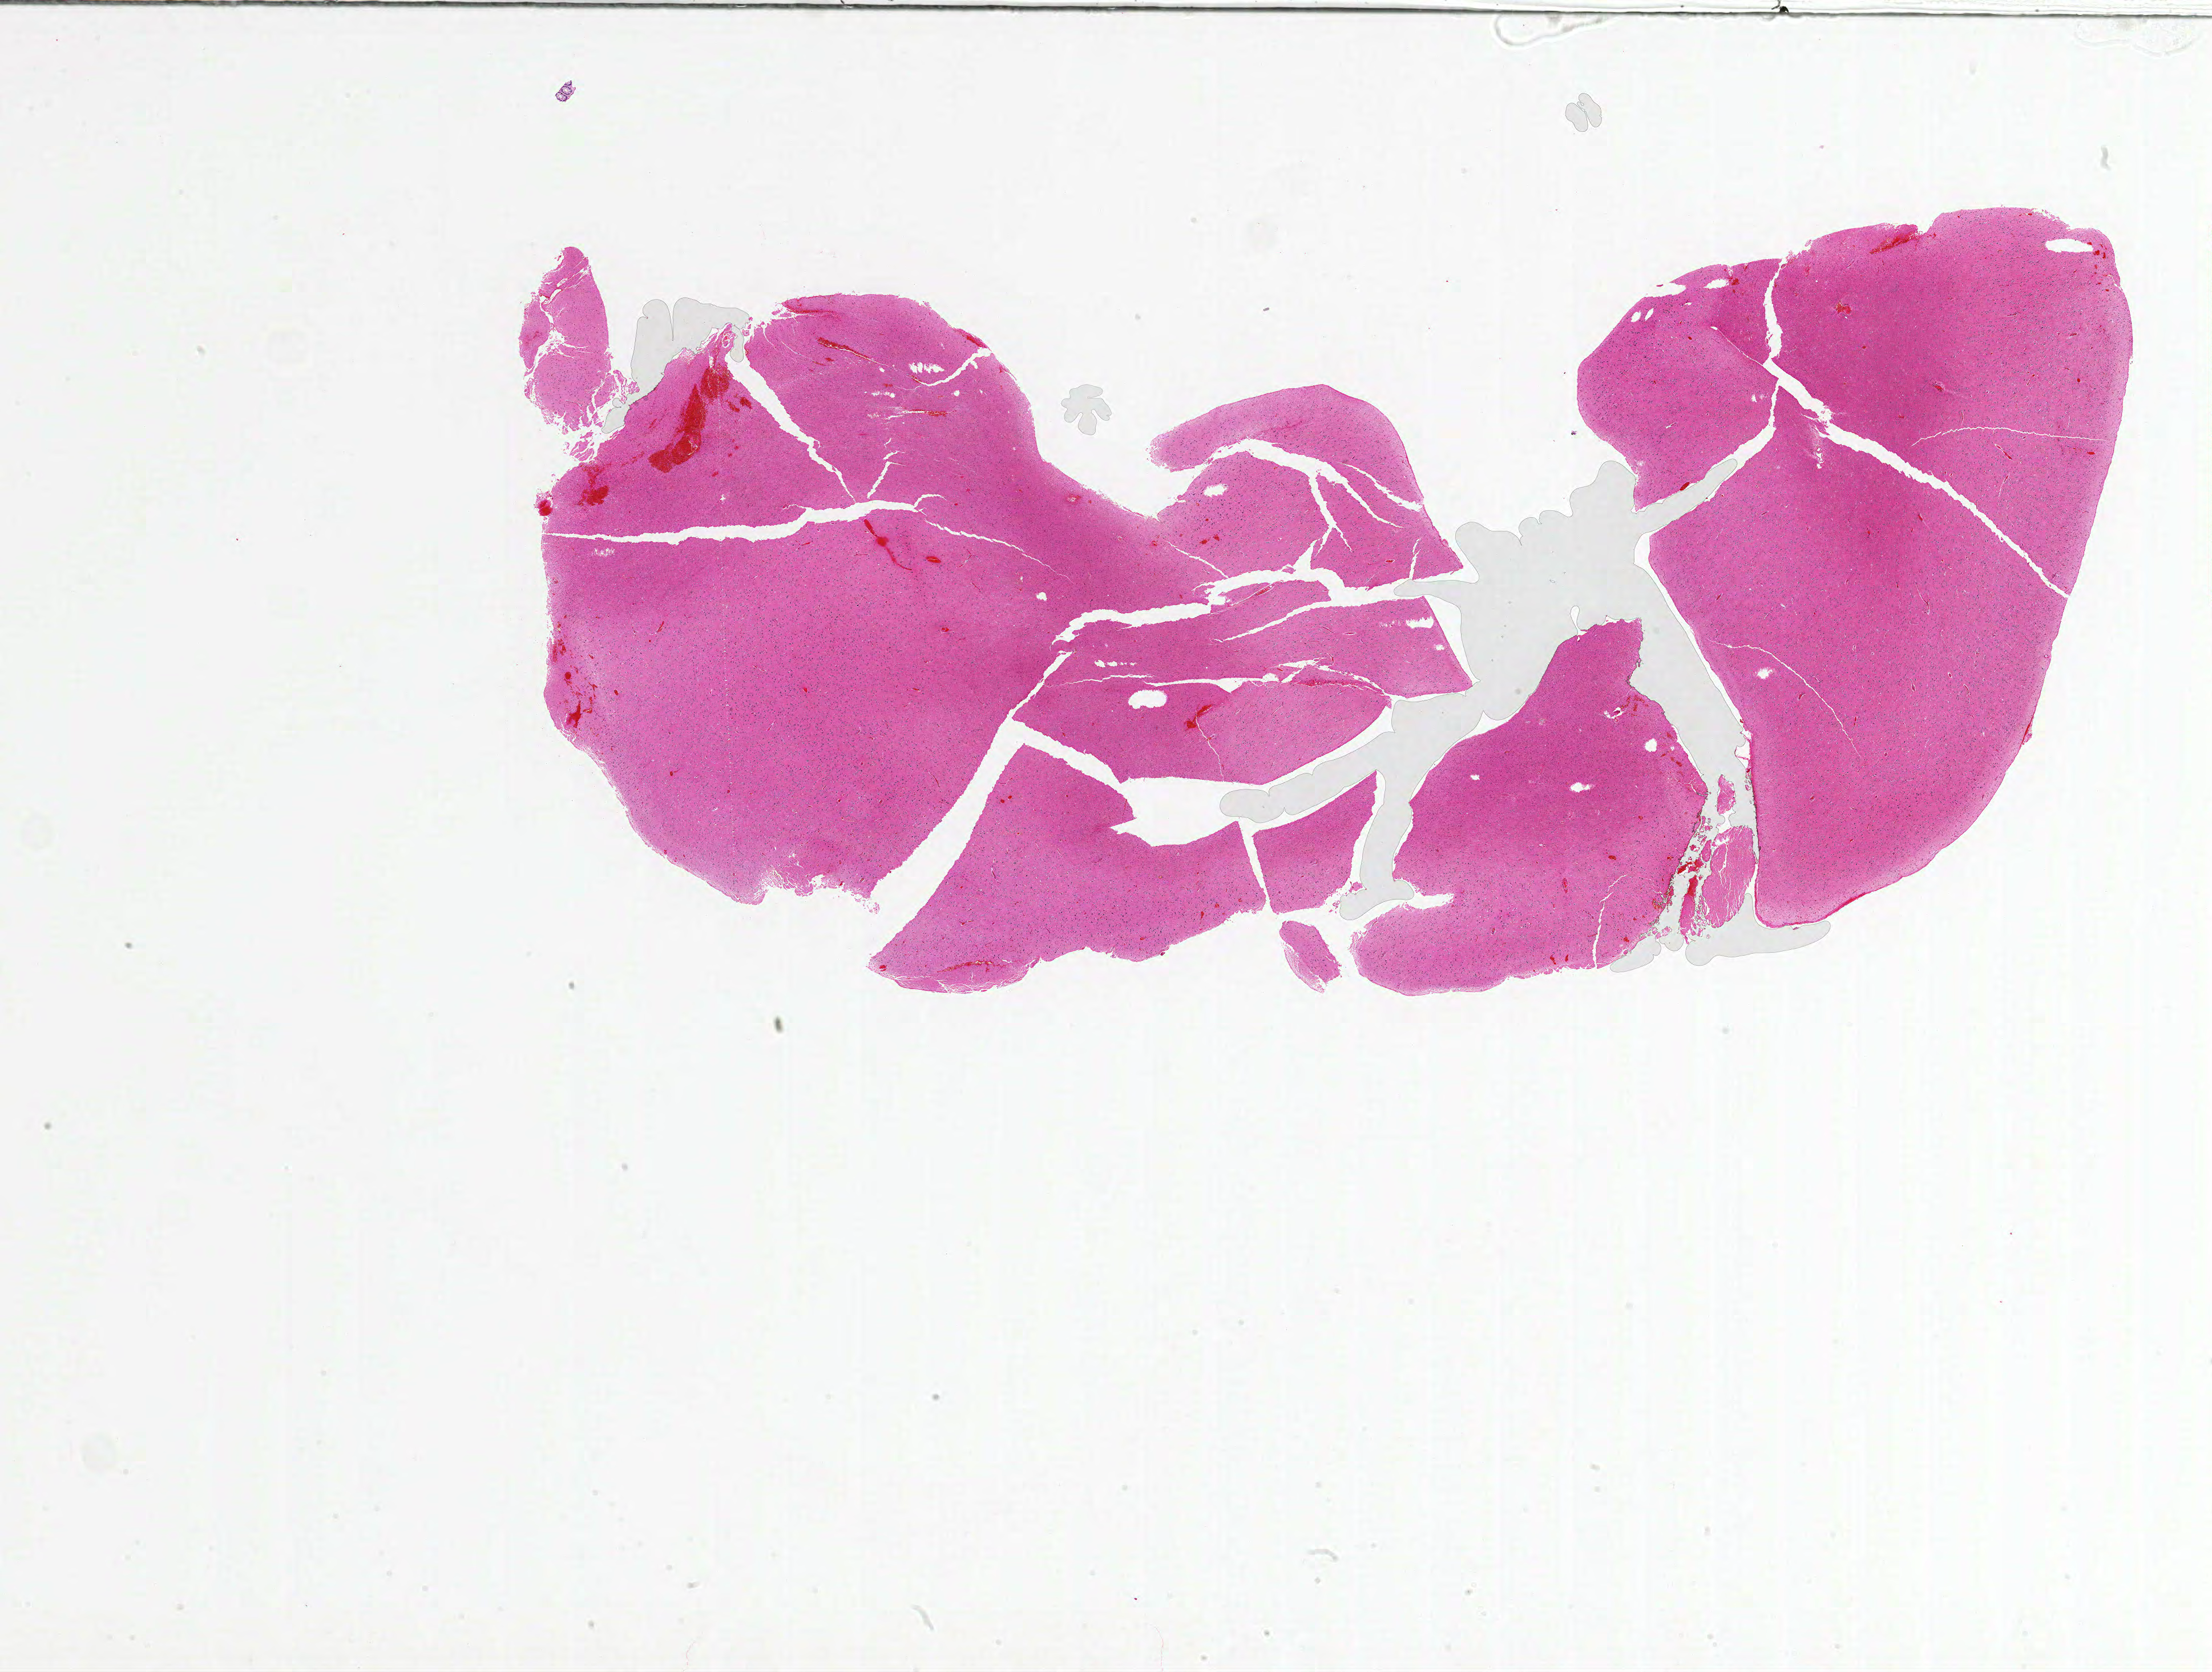
Digitized H&E tissue section (whole slide), whole scanned area (about 31.0 x 23.4 mm, slide scanned at 20x) shown as a low-resolution overview, FFPE section, brain, primary tumour sample. Male patient; age at initial diagnosis 58 years.
Diagnosis: Glioblastoma.